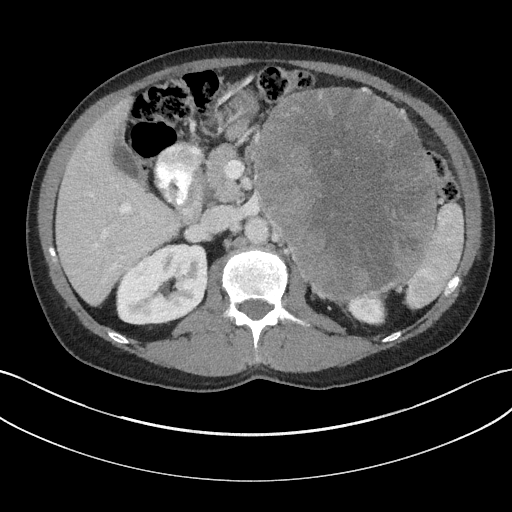
Contrast-enhanced abdominal CT, one axial slice. Position 105 of 147 along the scan axis. Reconstruction kernel I31f/3. Intravenous contrast given. Soft-tissue window (W 400 / L 40 HU). 3 mm slice thickness. 512 × 512 image matrix. Male patient, age 58 years. From the clinical record (not read from this slice): diagnosis: adrenocortical carcinoma; tumour side: left adrenal; tumour size at pathology: 22 cm; Ki-67 index: 26 %.
Structures marked on this image (semi-automatic segmentation, software-assisted and operator-edited):
- mass: bounding box <258,89,436,299> (left, top, right, bottom; pixels)